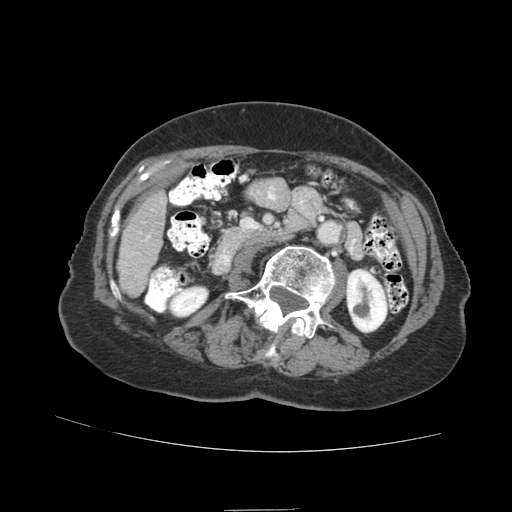
Contrast-enhanced abdominal CT (liver protocol), one axial slice. Position 20 of 89 along the scan axis. Reconstruction kernel STANDARD. 140 kVp. Soft-tissue window (W 400 / L 40 HU). 512 × 512 image matrix, field of view 360 × 360 mm. Case-level facts recorded for this patient, not image findings: diagnosis: hepatocellular carcinoma (patient treated with transarterial chemoembolisation; whether this scan precedes or follows treatment is not stated here); TNM stage (as recorded): Stage-II; Child-Pugh class: A; tumour differentiation: moderately differentiated; tumour nodularity: multinodular.
Structures marked on this image (semi-automatically segmented with operator editing):
- liver parenchyma outside the tumour (the mass and vessels are separate outlines, so this box may not span the whole liver): bounding box (x1, y1, x2, y2) in pixels: (116, 190, 166, 297)
- liver vessels: (145, 236, 150, 240)